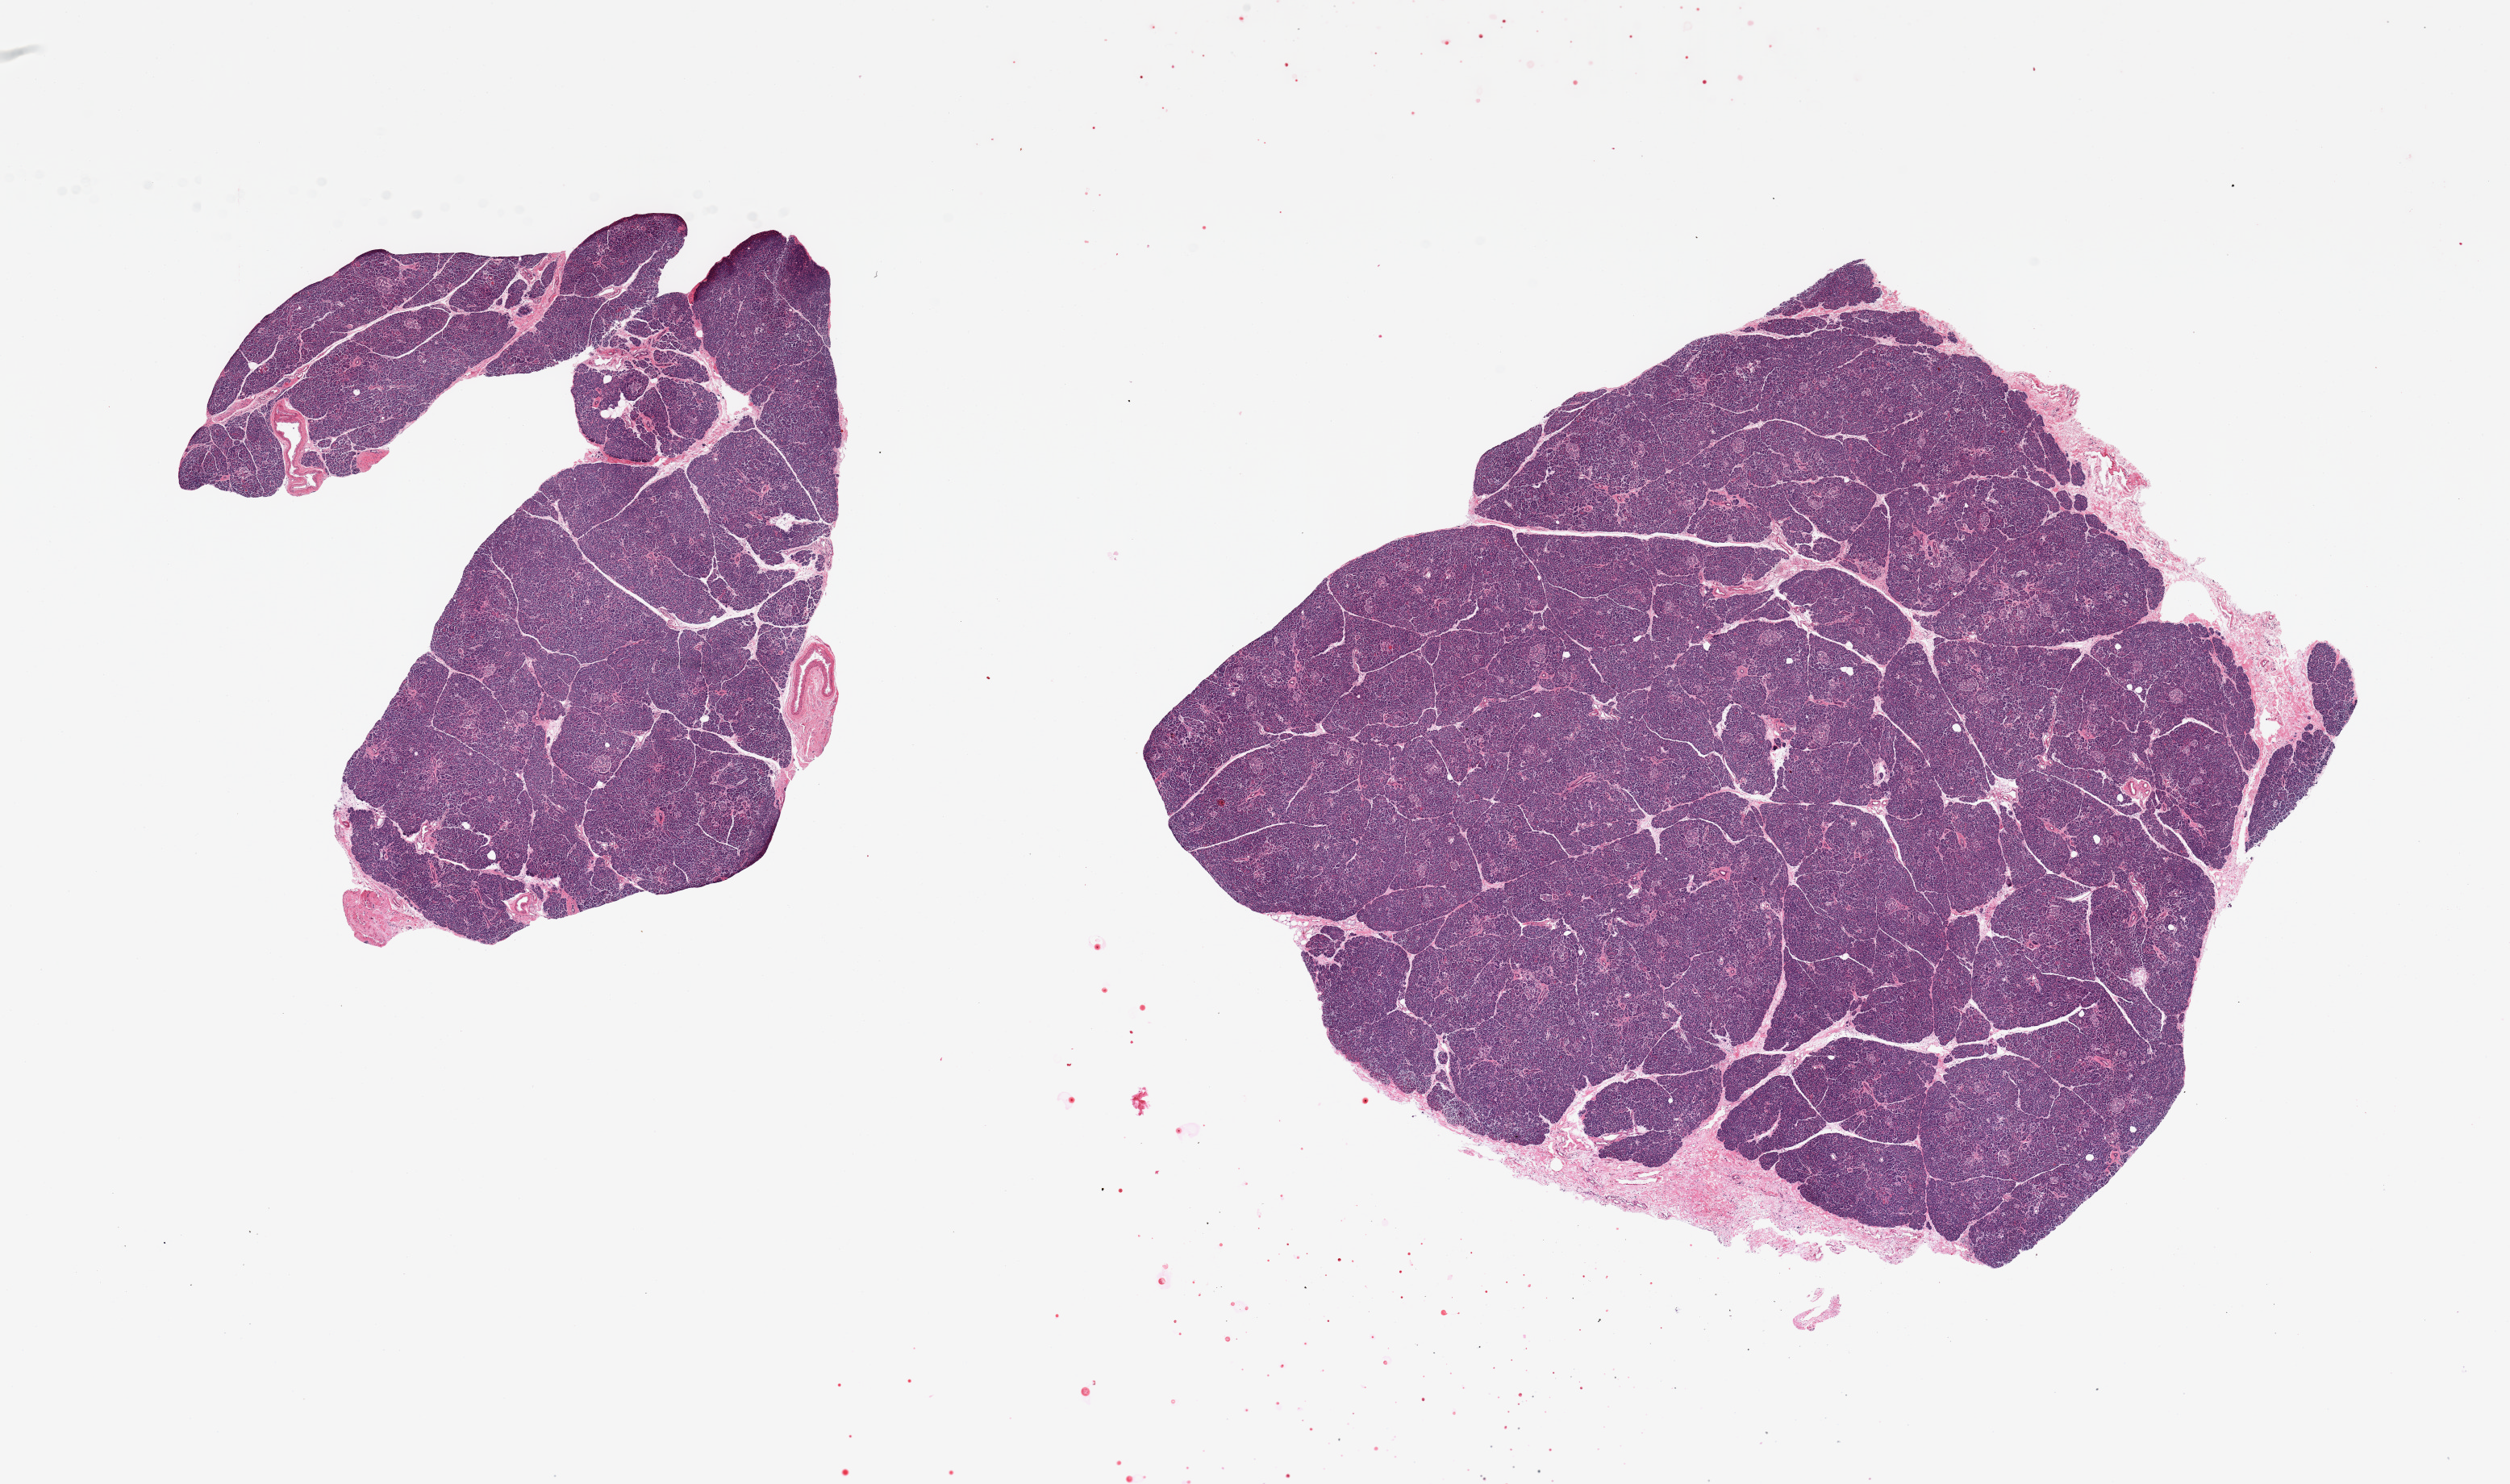
H&E whole-slide image, a low-resolution overview of the entire scanned area, about 24.6 x 14.6 mm (from a 20x scan). PAXgene-fixed, paraffin-embedded tissue. Section of pancreas (target tissue). Donor tissue sample.
Review note (as recorded): 2 pieces; islets are well visualized.